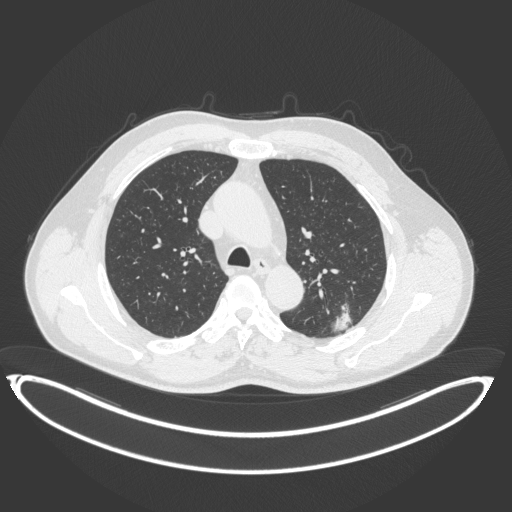
Chest CT, one axial slice; 120 kVp; lung window (W 1500 / L -600 HU); 512 × 512 image matrix. Male patient, age 58 years. From the clinical record (not read from this slice): clinical TNM (as recorded): T1c N0 M0.
Structures marked on this image (rectangle marked by the reading radiologist):
- lung tumour (recorded histology: adenocarcinoma): box from (x=331, y=303) to (x=357, y=336) px